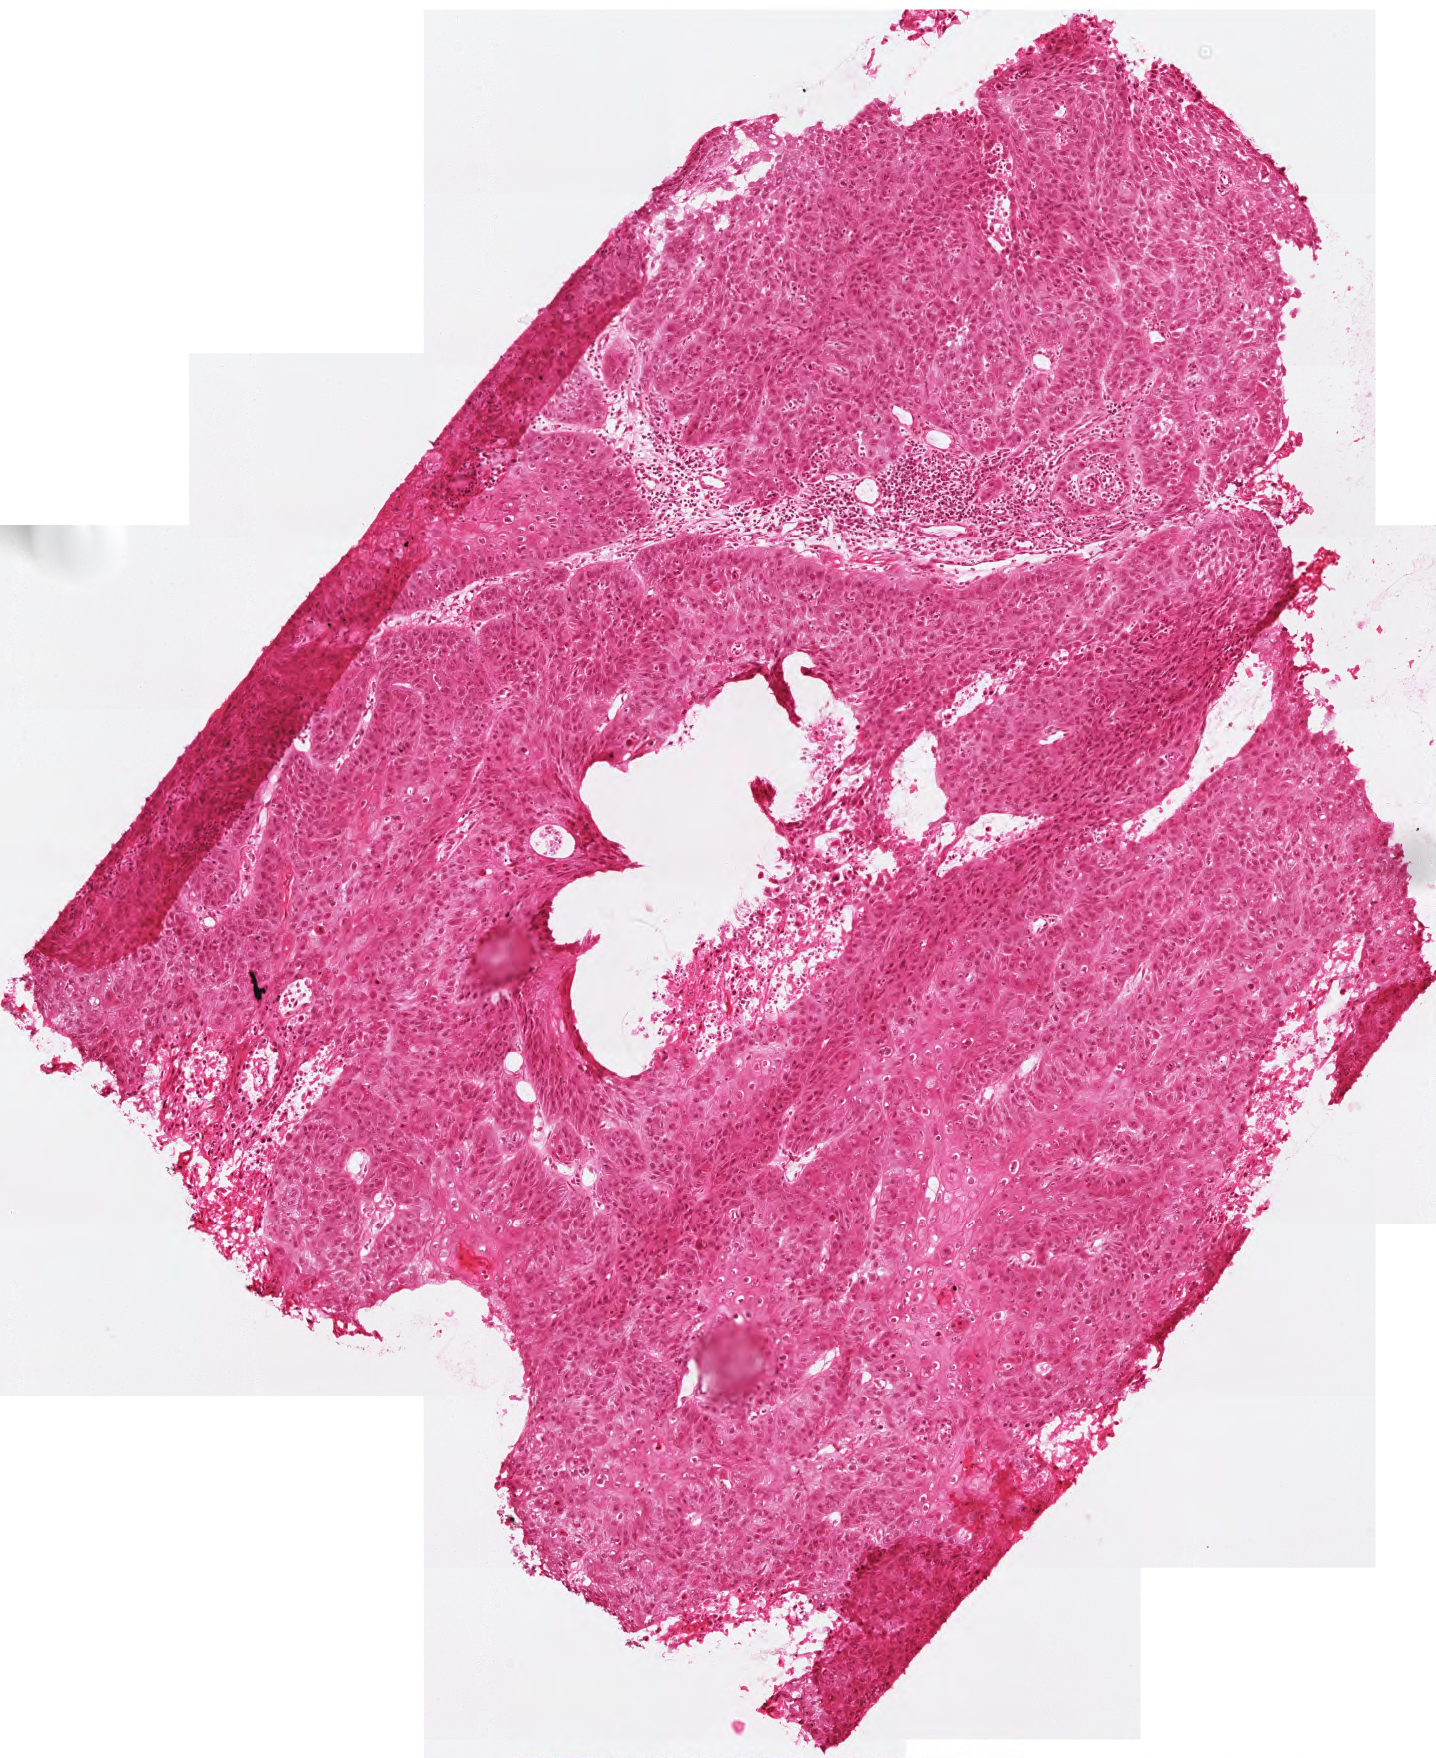
Whole-slide histology image, H&E-stained, shown as a low-resolution overview of the whole scanned area (about 2.9 x 3.5 mm), frozen section from the top of the tissue portion, primary tumour sample from the head and neck. Patient: male, age at initial diagnosis 69 years. Histologic grade: G2 (moderately differentiated). Composition of this section per pathologist review: tumour cells 95%, tumour nuclei 90%, normal cells 0%, stromal cells 5%, necrosis 0%.
AJCC pathologic stage: IVA (7th edition). Pathologic diagnosis: Squamous cell carcinoma, NOS. TNM: T3 N2b.